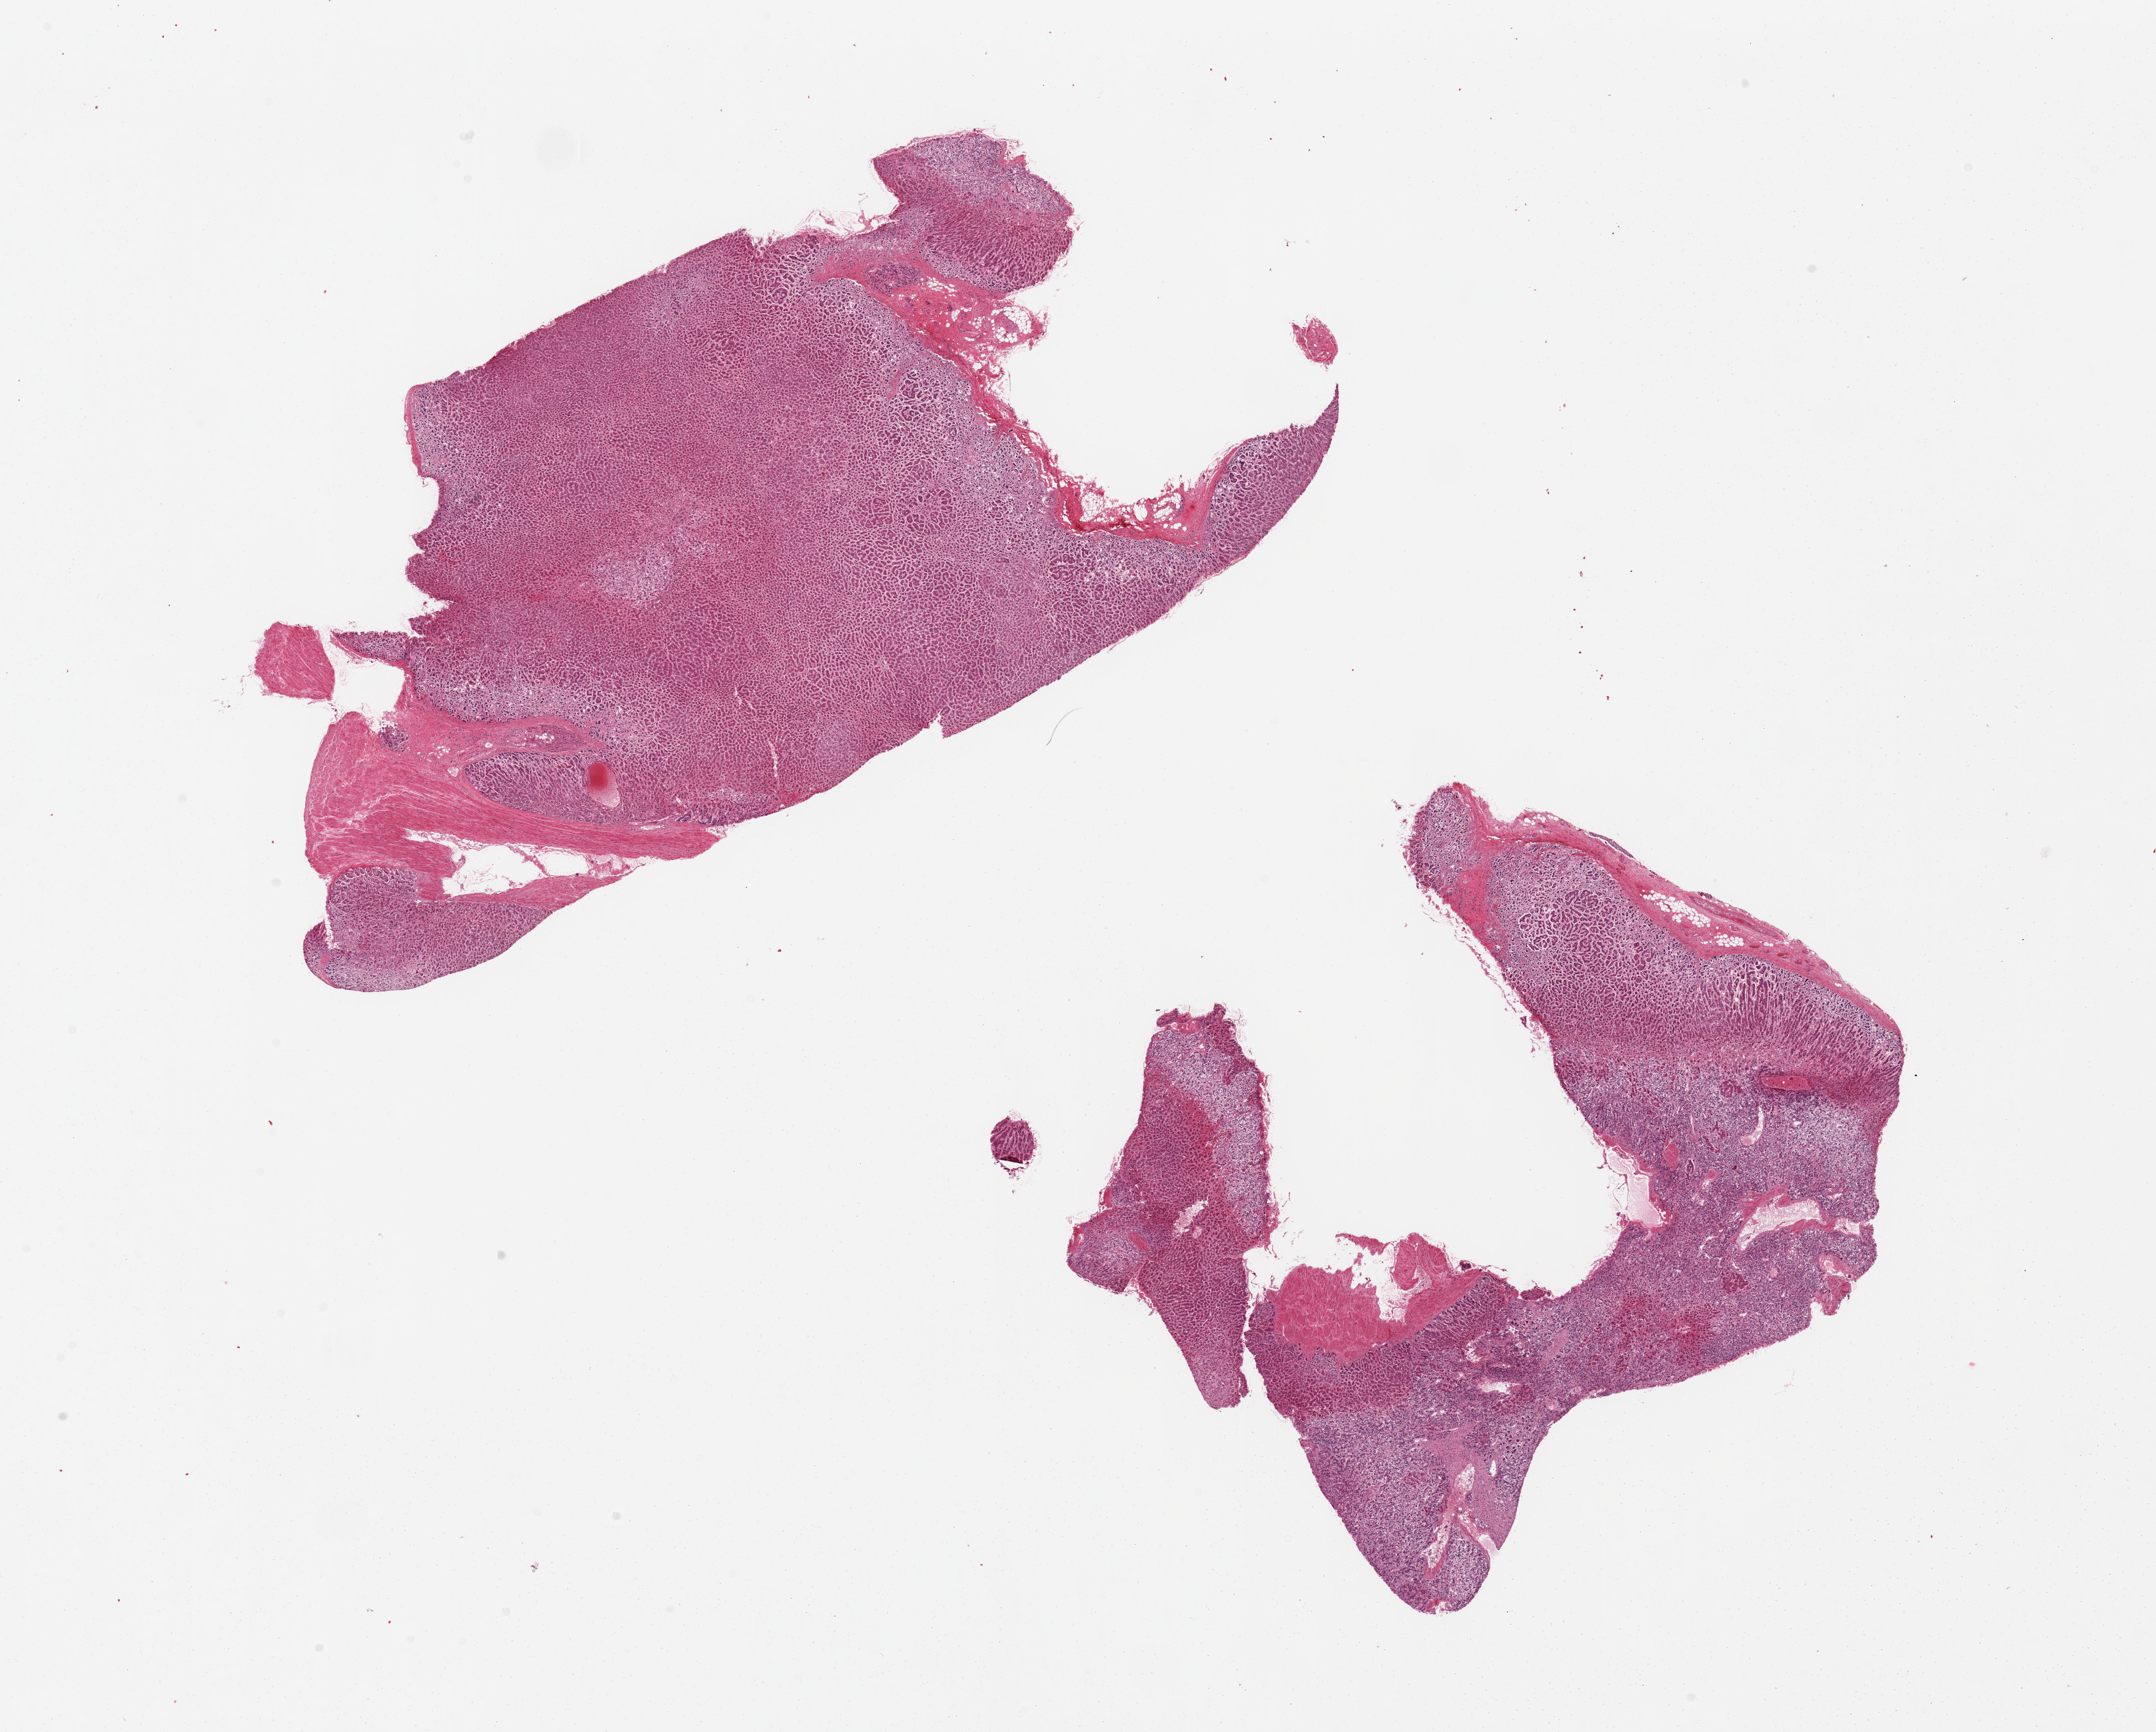
Digitized haematoxylin and eosin-stained section, shown as a low-resolution overview of the whole scanned area (about 25.6 x 20.6 mm, from a 20x scan), PAXgene-fixed paraffin-embedded (PFPE) section, sampled site (target tissue): adrenal gland, donor tissue sample.
Review note (as recorded): 2 pieces, all cortex, moderately autolyzed.